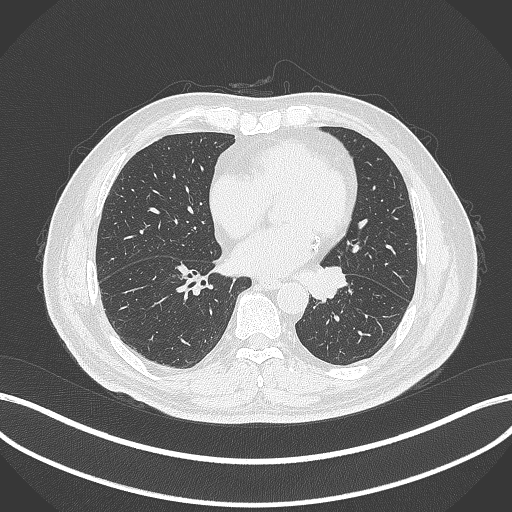
Chest CT, one axial slice; position 115 of 312 along the scan axis; reconstruction kernel B70f; lung window (W 1500 / L -600 HU); 1 mm slice thickness; 512 × 512 image matrix. Patient: male, 71 years. Case-level facts recorded for this patient, not image findings: clinical TNM (as recorded): T1b N0 M0.
Structures marked on this image (rectangle marked by the reading radiologist):
- lung tumour (recorded histology: squamous cell carcinoma): bounding box [x1, y1, x2, y2] px = [310, 263, 347, 302]